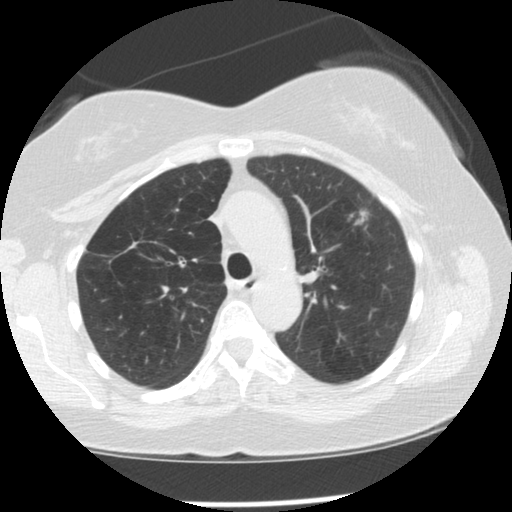
Chest CT (low-dose screening protocol), one axial image; second screening round (one year after baseline); lung window (W 1500 / L -600 HU); 2.5 mm slice thickness; standard (soft-tissue) reconstruction kernel (STANDARD); slice 39 of 128 in the series. Female, age 57 years at enrolment. Former smoker at enrolment.
- Expert reader's lesion annotation, bounding box (x1, y1, x2, y2) in pixels: (338, 200, 378, 234).
- Screening reader's record for this exam (one nodule recorded; not confirmed to be the boxed lesion): non-calcified nodule or mass ≥4 mm, left upper lobe, 11 × 7 mm, spiculated (stellate) margins, soft tissue attenuation, pre-existing on the prior screen: yes; interval growth: yes.
- Official screen result: positive, change unspecified: nodule(s) >= 4 mm or enlarging nodule(s), mass(es), or other non-specific abnormalities suspicious for lung cancer.